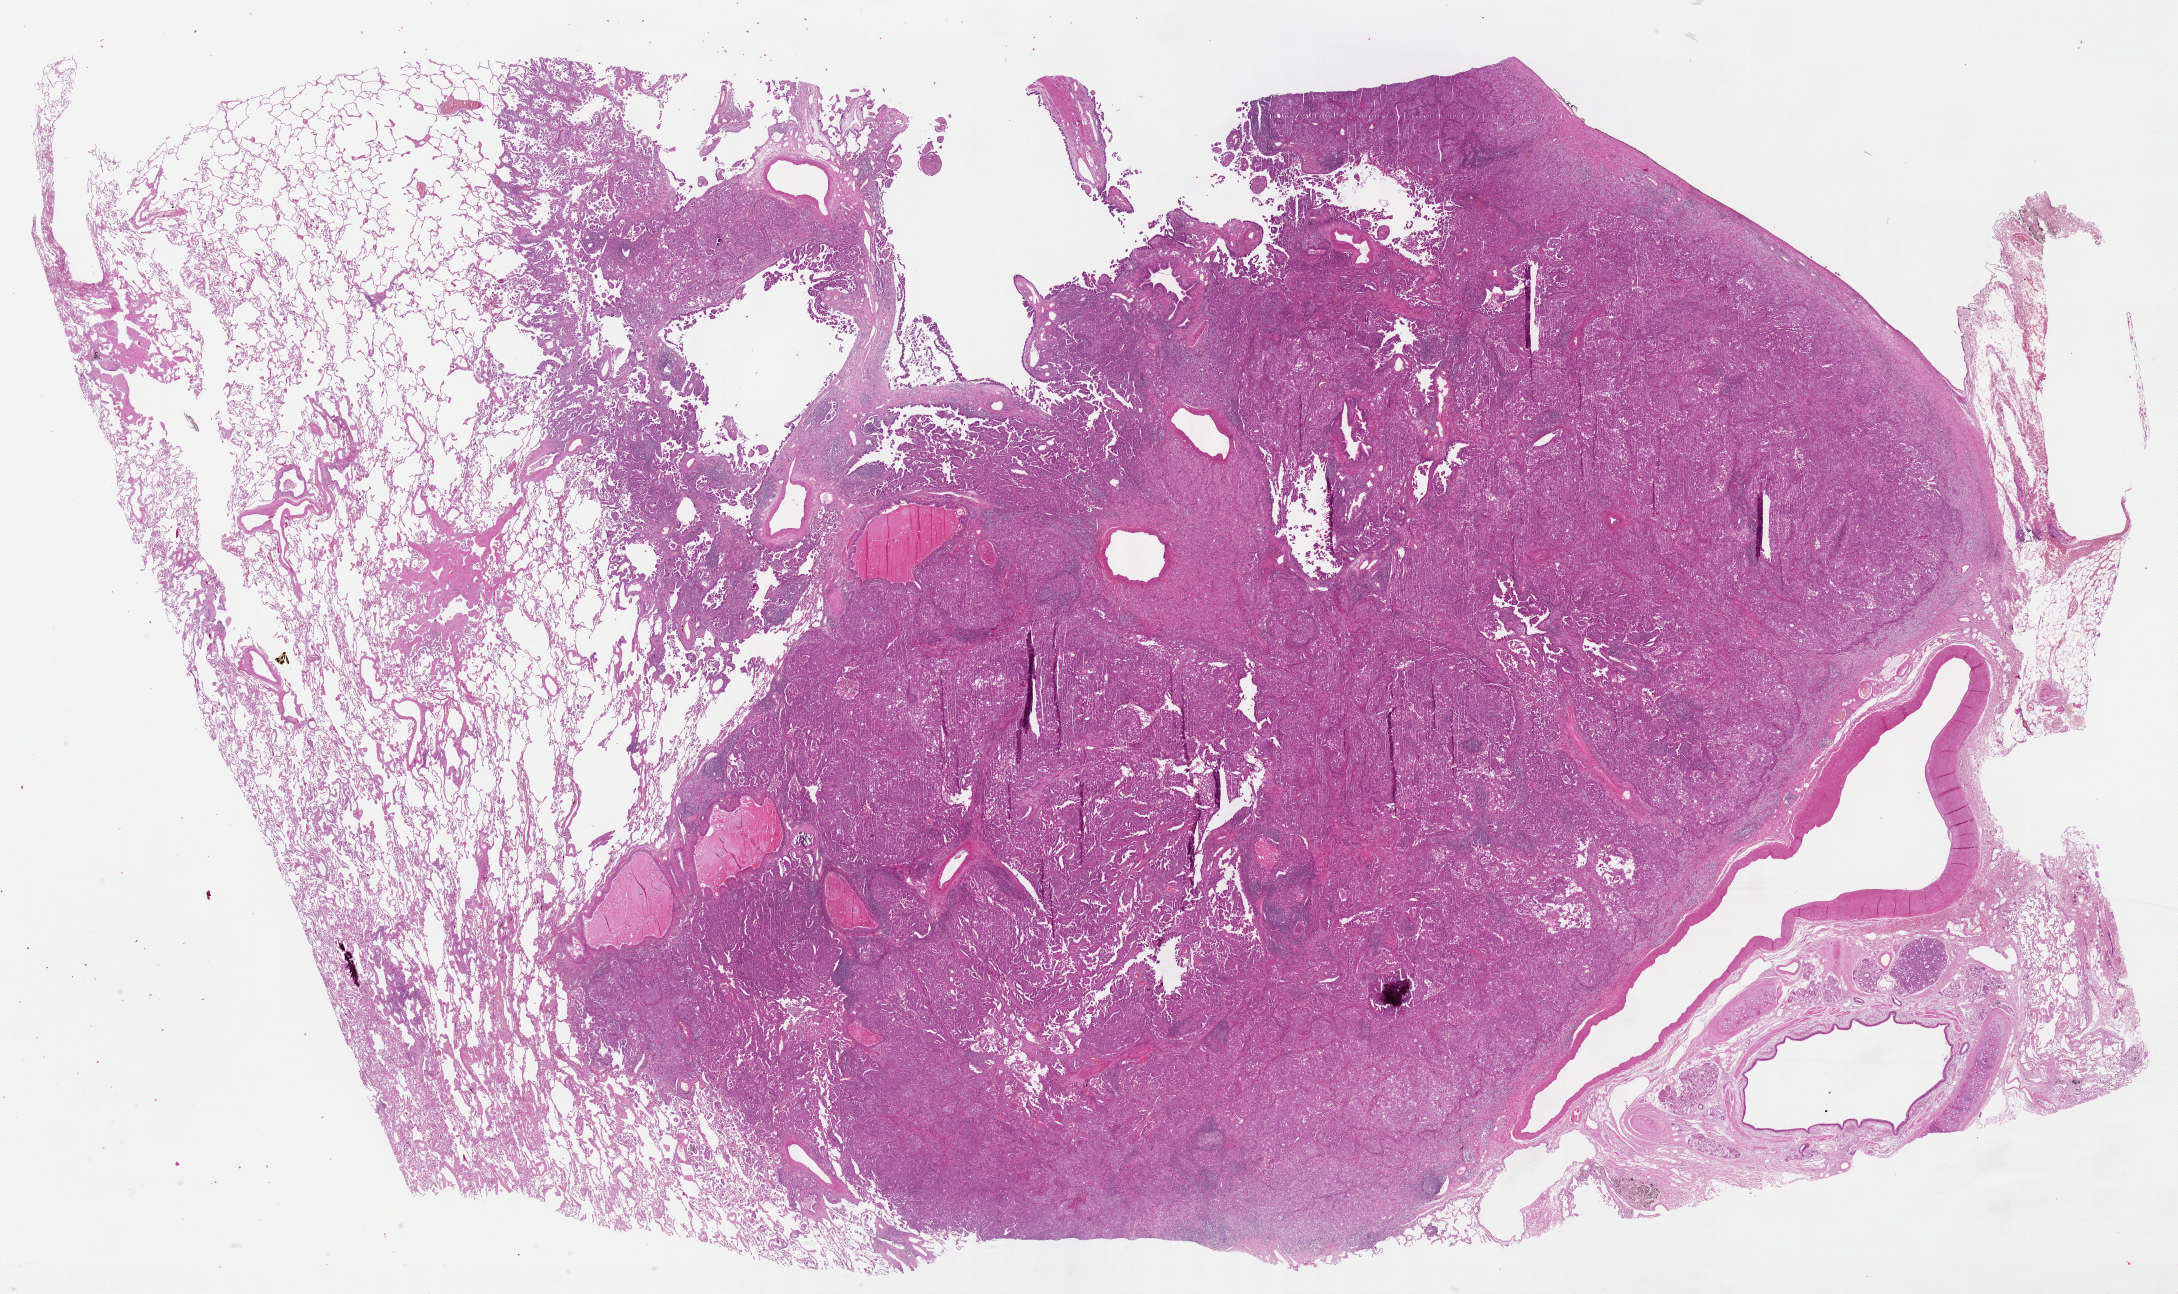
Digitized H&E-stained tissue section (whole slide), a low-resolution overview of the entire scanned area, about 35.2 x 20.9 mm (slide scanned at 40x). Formalin-fixed paraffin-embedded (FFPE) diagnostic section. Lung, primary tumour sample. Male patient; age at initial diagnosis 70 years.
* laterality: right
* histologic diagnosis: Squamous cell carcinoma, keratinizing, NOS (middle lobe, lung)
* AJCC pathologic stage: IIIA (7th edition)